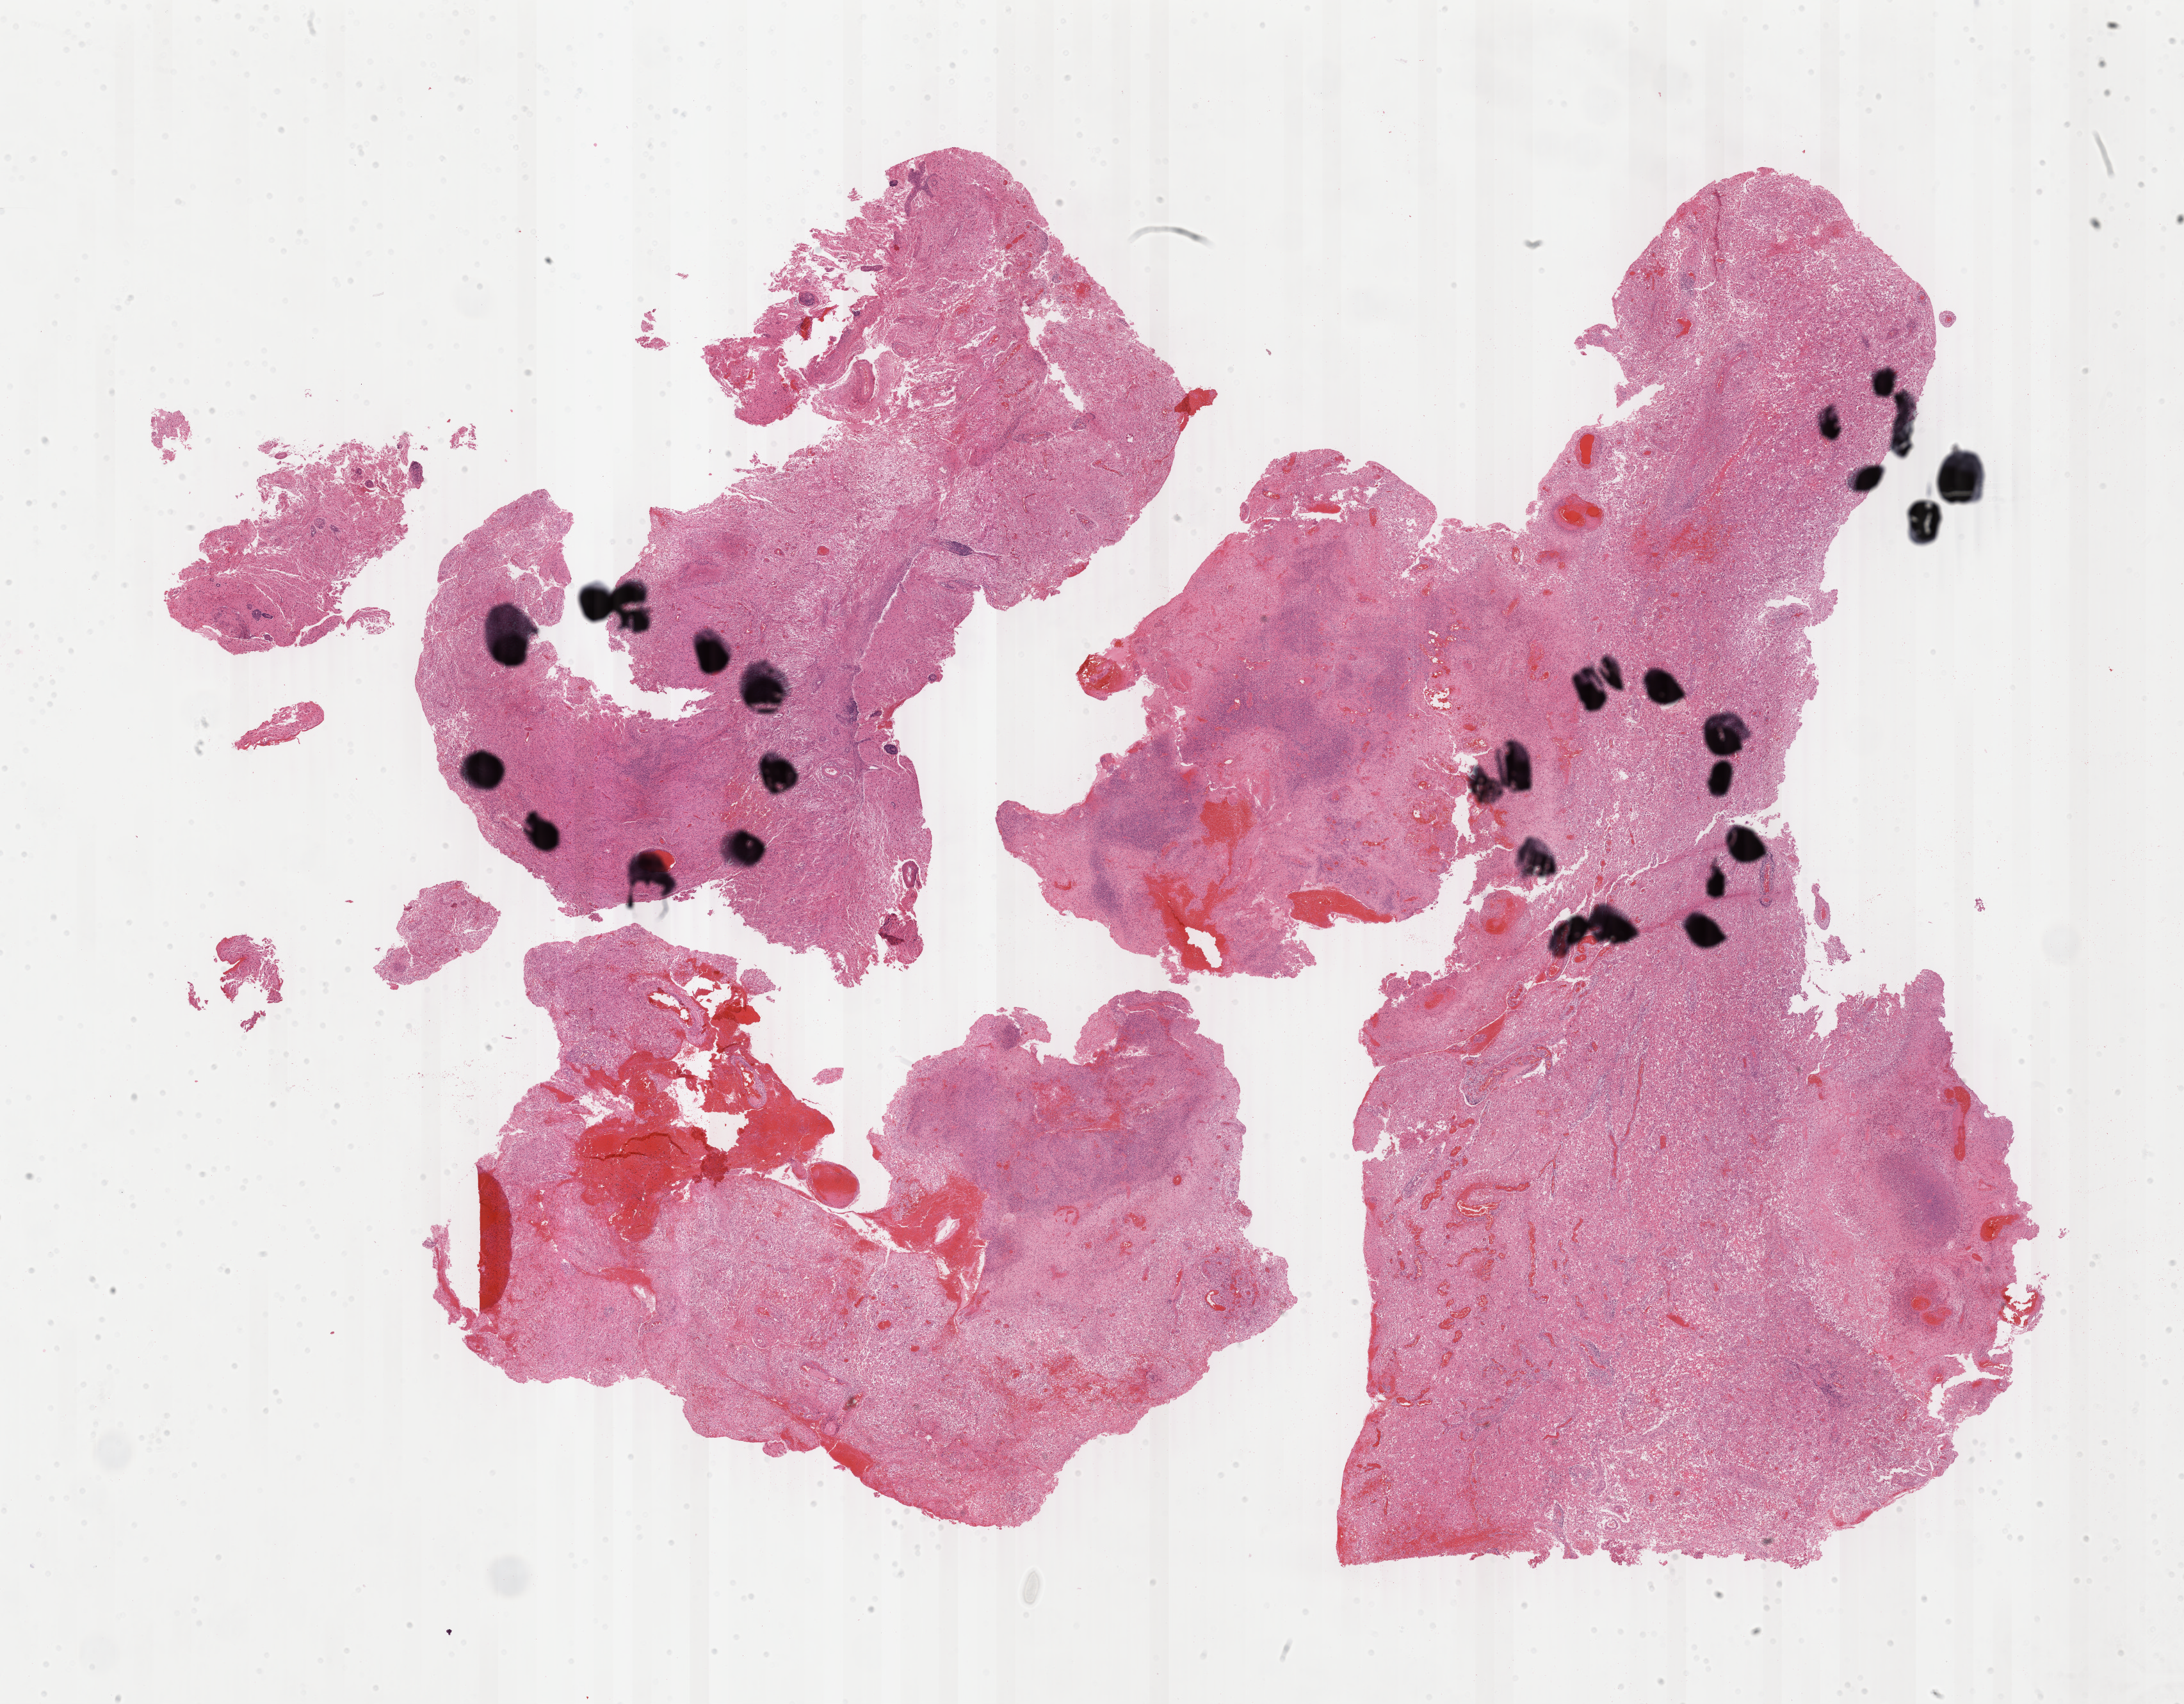
Digitized Hematoxylin and eosin (H&E) stained tissue section (whole slide), a low-resolution overview of the entire scanned area, about 27.1 x 21.2 mm; FFPE section; brain, primary tumour sample. Patient: male, age at initial diagnosis 36 years.
Diagnosis: Glioblastoma.